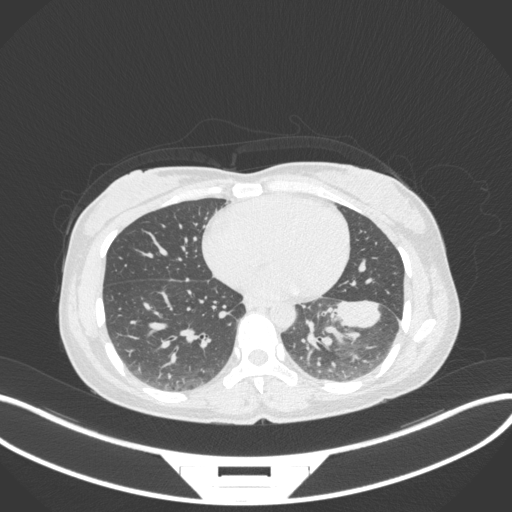
Chest CT, one axial slice; position 142 of 361 along the scan axis; reconstruction kernel B31f; lung window (W 1500 / L -600 HU); 1 mm slice thickness; 512 × 512 image matrix. Female patient, age 41 years. From the clinical record (not read from this slice): clinical TNM (as recorded): T2a N3 M1b.
Outlined on this slice (rectangle marked by the reading radiologist):
- lung tumour (recorded histology: adenocarcinoma): bounding box <325,293,391,332> (left, top, right, bottom; pixels)